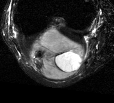
MRI of an extremity soft-tissue mass, one axial slice; position 17 of 44 along the scan axis; T2-weighted fat-saturated; MR volume resampled by the dataset authors to the PET/CT grid (not the native acquisition matrix); 114 × 103 image matrix, field of view 111 × 101 mm. Female patient. Case-level facts recorded for this patient, not image findings: histological type: liposarcoma; site of the primary tumour: right thigh.
Annotated regions visible in this slice (expert contour drawn on MRI and transferred to this co-registered scan by the dataset authors):
- gross tumour volume (mass): bounding box (x1, y1, x2, y2) in pixels: (29, 25, 87, 81)